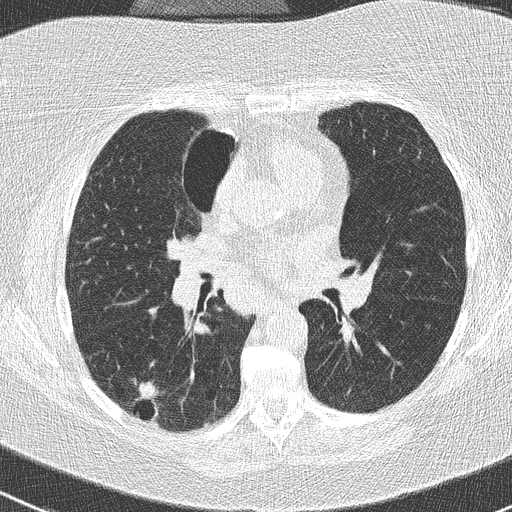
Low-dose screening chest CT, one axial slice. Slice 140 of 261 in the series (ordered by position). 120 kVp. Lung window (W 1500 / L -600 HU). 2 mm slice thickness. 512 × 512 image matrix, field of view 310 × 310 mm.
Annotated regions visible in this slice (manually delineated by an expert):
- lesion 1 (tumor, lower lobe of right lung): bounding box <135,381,159,401> (left, top, right, bottom; pixels)